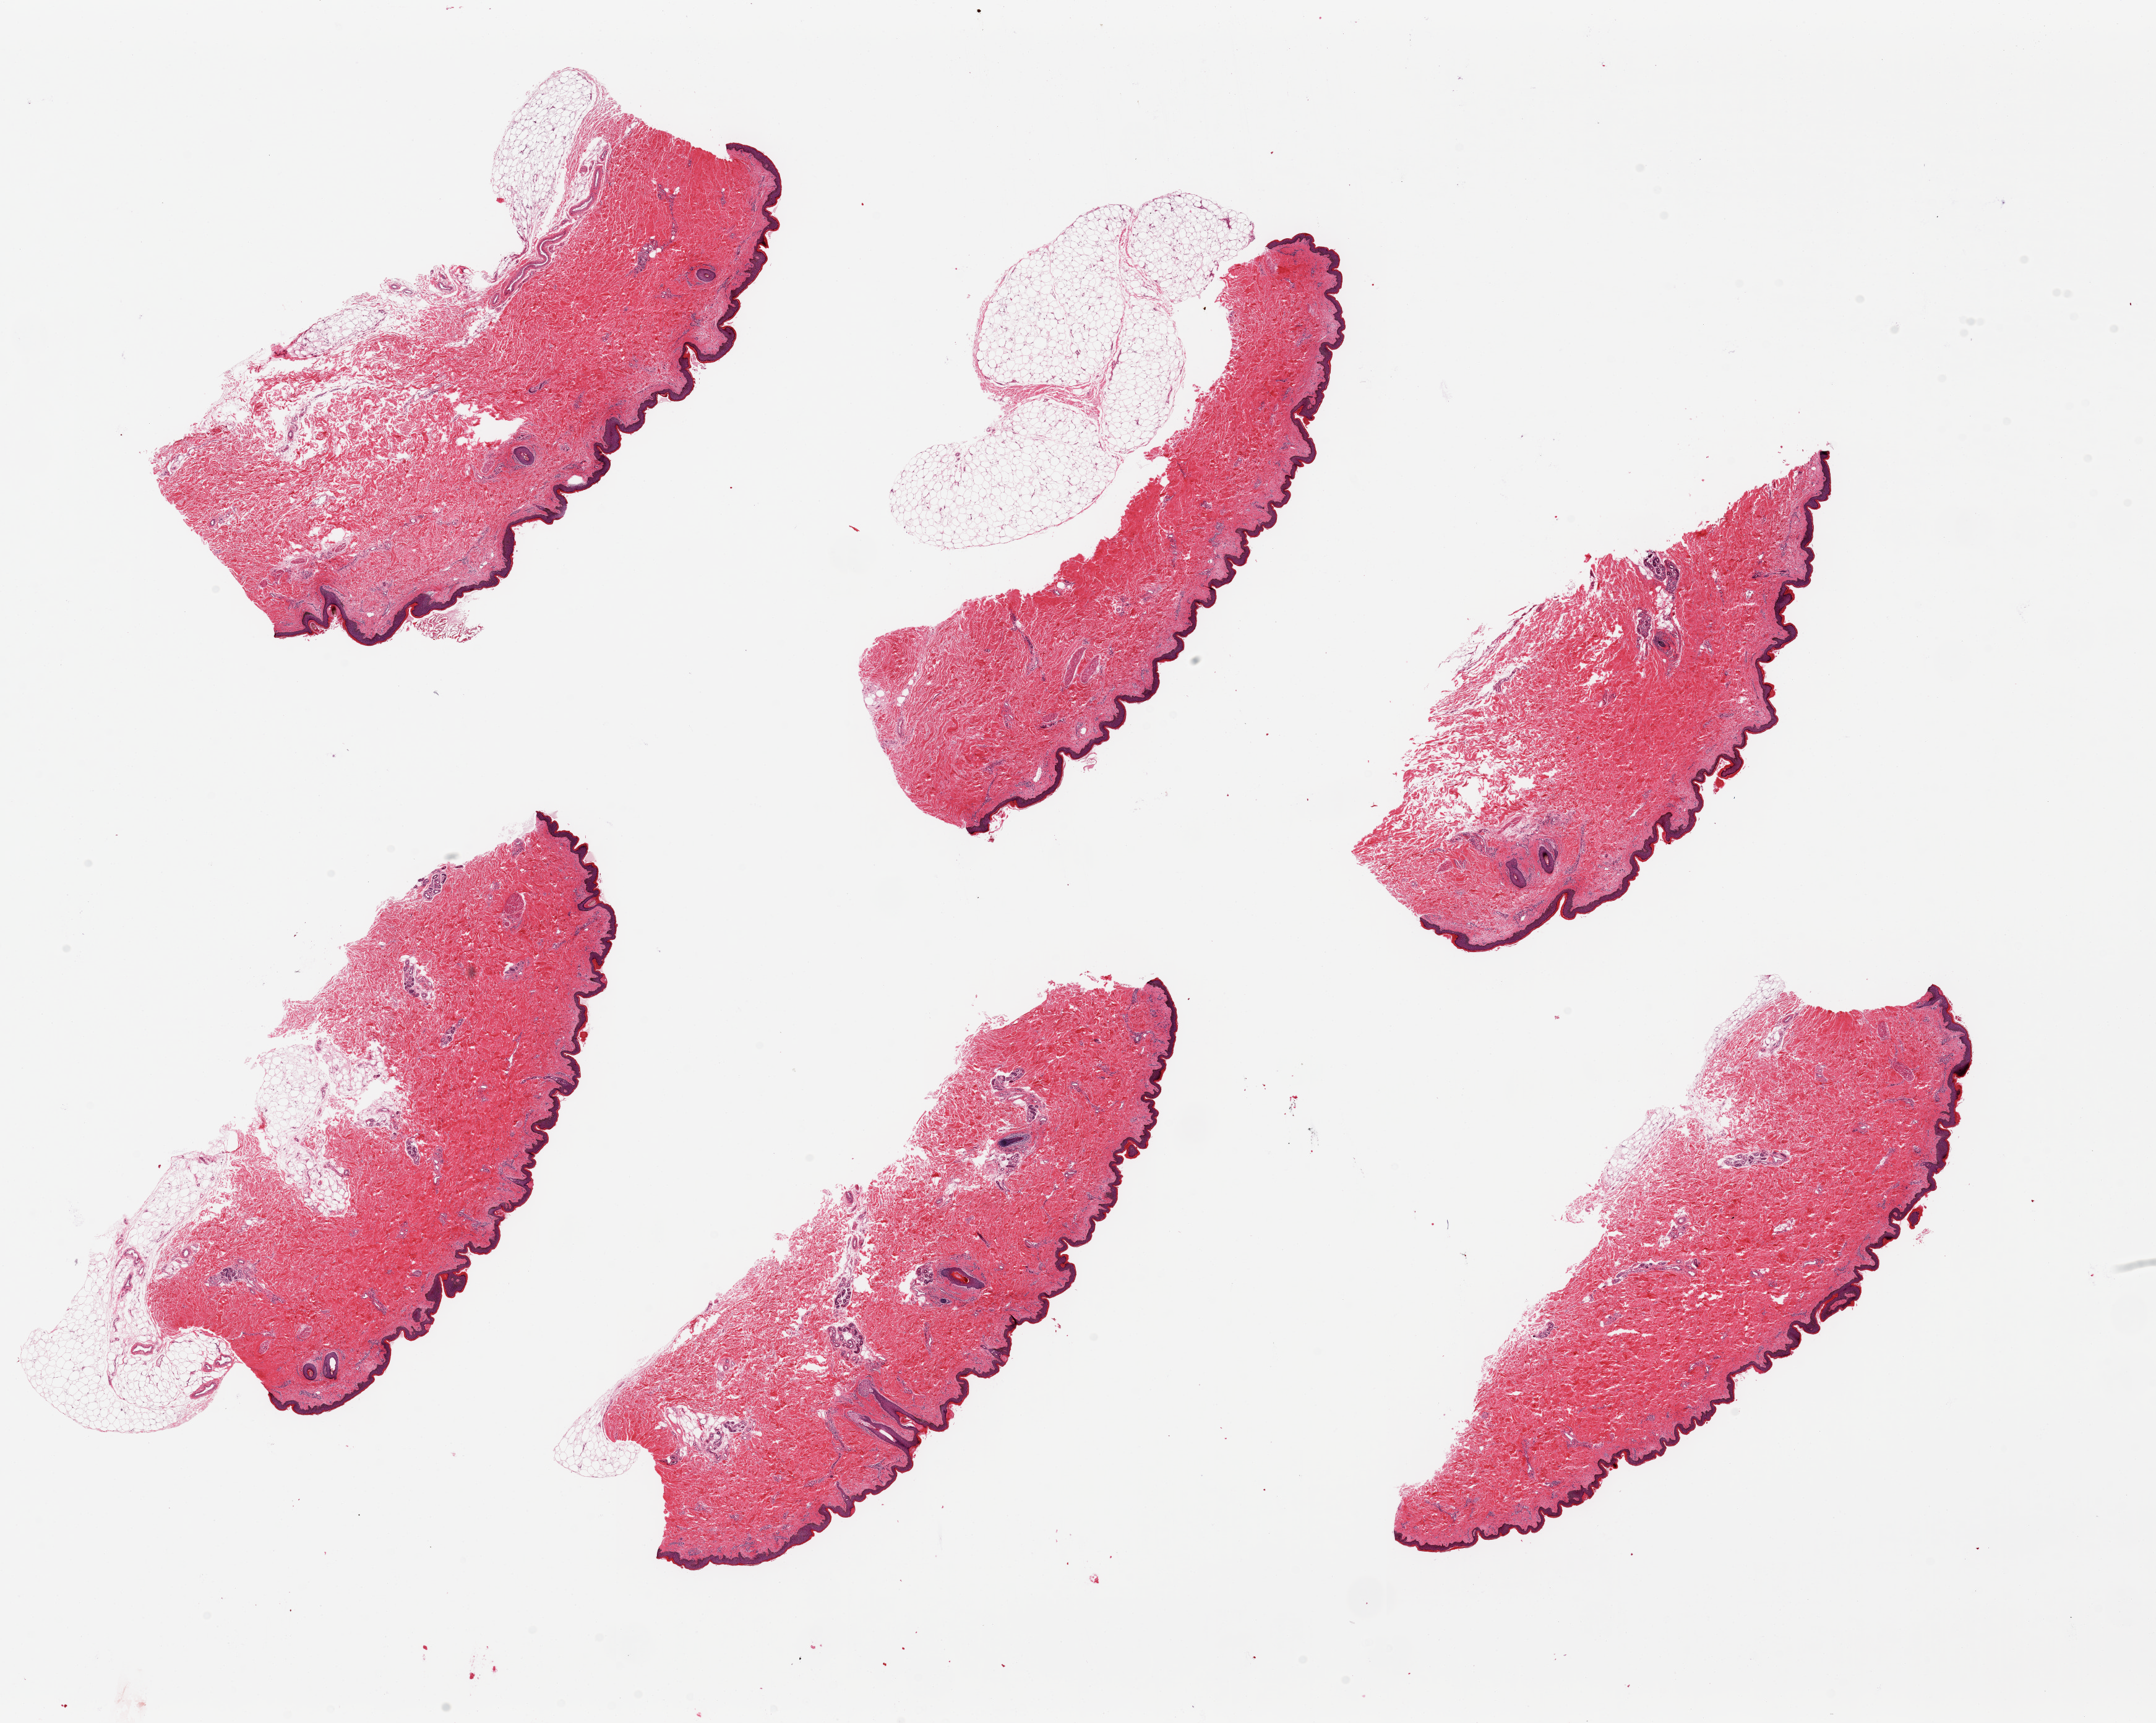
H&E whole-slide image, brightfield — shown as a low-resolution overview of the whole scanned area (about 27.6 x 22.0 mm, acquisition: 20x scan). PAXgene-fixed, paraffin-embedded tissue. Section of skin of lower leg (target tissue). Donor tissue sample. Male donor.
Review note (as recorded): 6 pieces ~8x4mm; Squamous epithelium is ~2% thickness; Small nubbins of adherent fat.